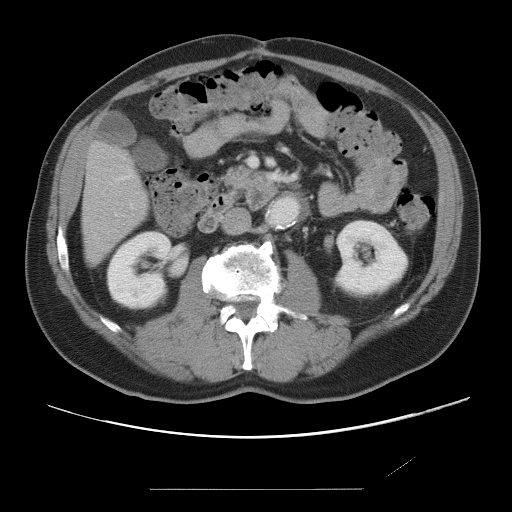
Contrast-enhanced abdominal CT, one axial slice. Slice 19 of 87 in the series (ordered by position). Intravenous contrast given. Soft-tissue window (W 400 / L 40 HU). 5 mm slice thickness. 512 × 512 image matrix, field of view 406 × 406 mm. Male patient, age 74 years. From the clinical record (not read from this slice): diagnosis: colorectal cancer liver metastases, imaged before liver resection; multiple liver metastases: yes; largest metastasis: 1.1 cm.
Outlined on this slice (outlined manually by an expert reader):
- hepatic veins: box from (x=120, y=176) to (x=130, y=180) px
- liver: (x=83, y=145)–(x=147, y=262)
- planned liver remnant (the part of the liver to remain after resection): (x=83, y=145)–(x=147, y=261)